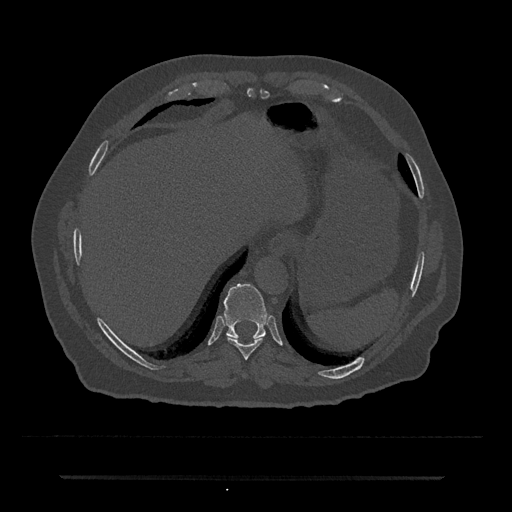
CT including the spine, one axial slice. Position 256 of 797 along the scan axis. 120 kVp. Bone window (W 1800 / L 400 HU). 512 × 512 image matrix. Male patient, age 69 years. From the clinical record (not read from this slice): primary cancer: prostate.
Annotated regions visible in this slice (semi-automatically segmented with operator editing):
- T10 vertebra: bounding box (x1, y1, x2, y2) in pixels: (223, 283, 267, 340)
- T9 vertebra: (227, 336, 264, 360)